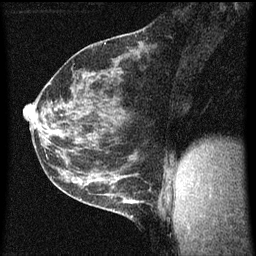
Breast MRI (dynamic contrast-enhanced), one sagittal slice. Slice 30 of 60 in the series (ordered by position). Dynamic contrast-enhanced series, image 2 of 3 at this slice position (ordered by acquisition). 1.5 T. TE 4.2 ms, TR 8 ms. 2 mm slice thickness. 256 × 256 image matrix, field of view 180 × 180 mm. Patient: female, 35 years.
Annotated regions visible in this slice (semi-automatically segmented with operator editing):
- analysis volume of interest (the breast-tissue region the enhancement analysis was run in; not a lesion): bounding box [x1, y1, x2, y2] px = [106, 182, 149, 223]
- tumour enhancement mask (voxels above the 70 % enhancement threshold inside the analysis volume of interest): [112, 188, 133, 219]